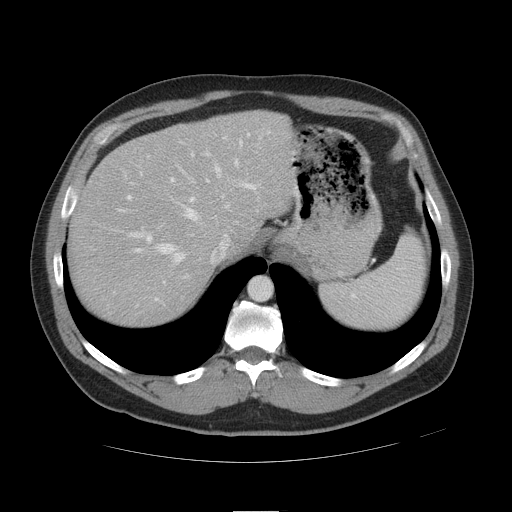
Contrast-enhanced abdominal CT, one axial slice. Position 36 of 49 along the scan axis. Reconstruction kernel STANDARD. 120 kVp. Intravenous contrast given. Soft-tissue window (W 400 / L 40 HU). 512 × 512 image matrix, field of view 425 × 425 mm. Male patient, age 52 years. Case-level facts recorded for this patient, not image findings: diagnosis: colorectal cancer liver metastases, imaged before liver resection; multiple liver metastases: yes; largest metastasis: 5.1 cm; disease in both lobes: yes.
Structures marked on this image (outlined manually by an expert reader):
- hepatic veins: bounding box (x1, y1, x2, y2) in pixels: (118, 136, 262, 301)
- liver: (70, 114, 289, 325)
- planned liver remnant (the part of the liver to remain after resection): (133, 114, 289, 244)
- portal vein (with intrahepatic branches): (124, 133, 259, 243)